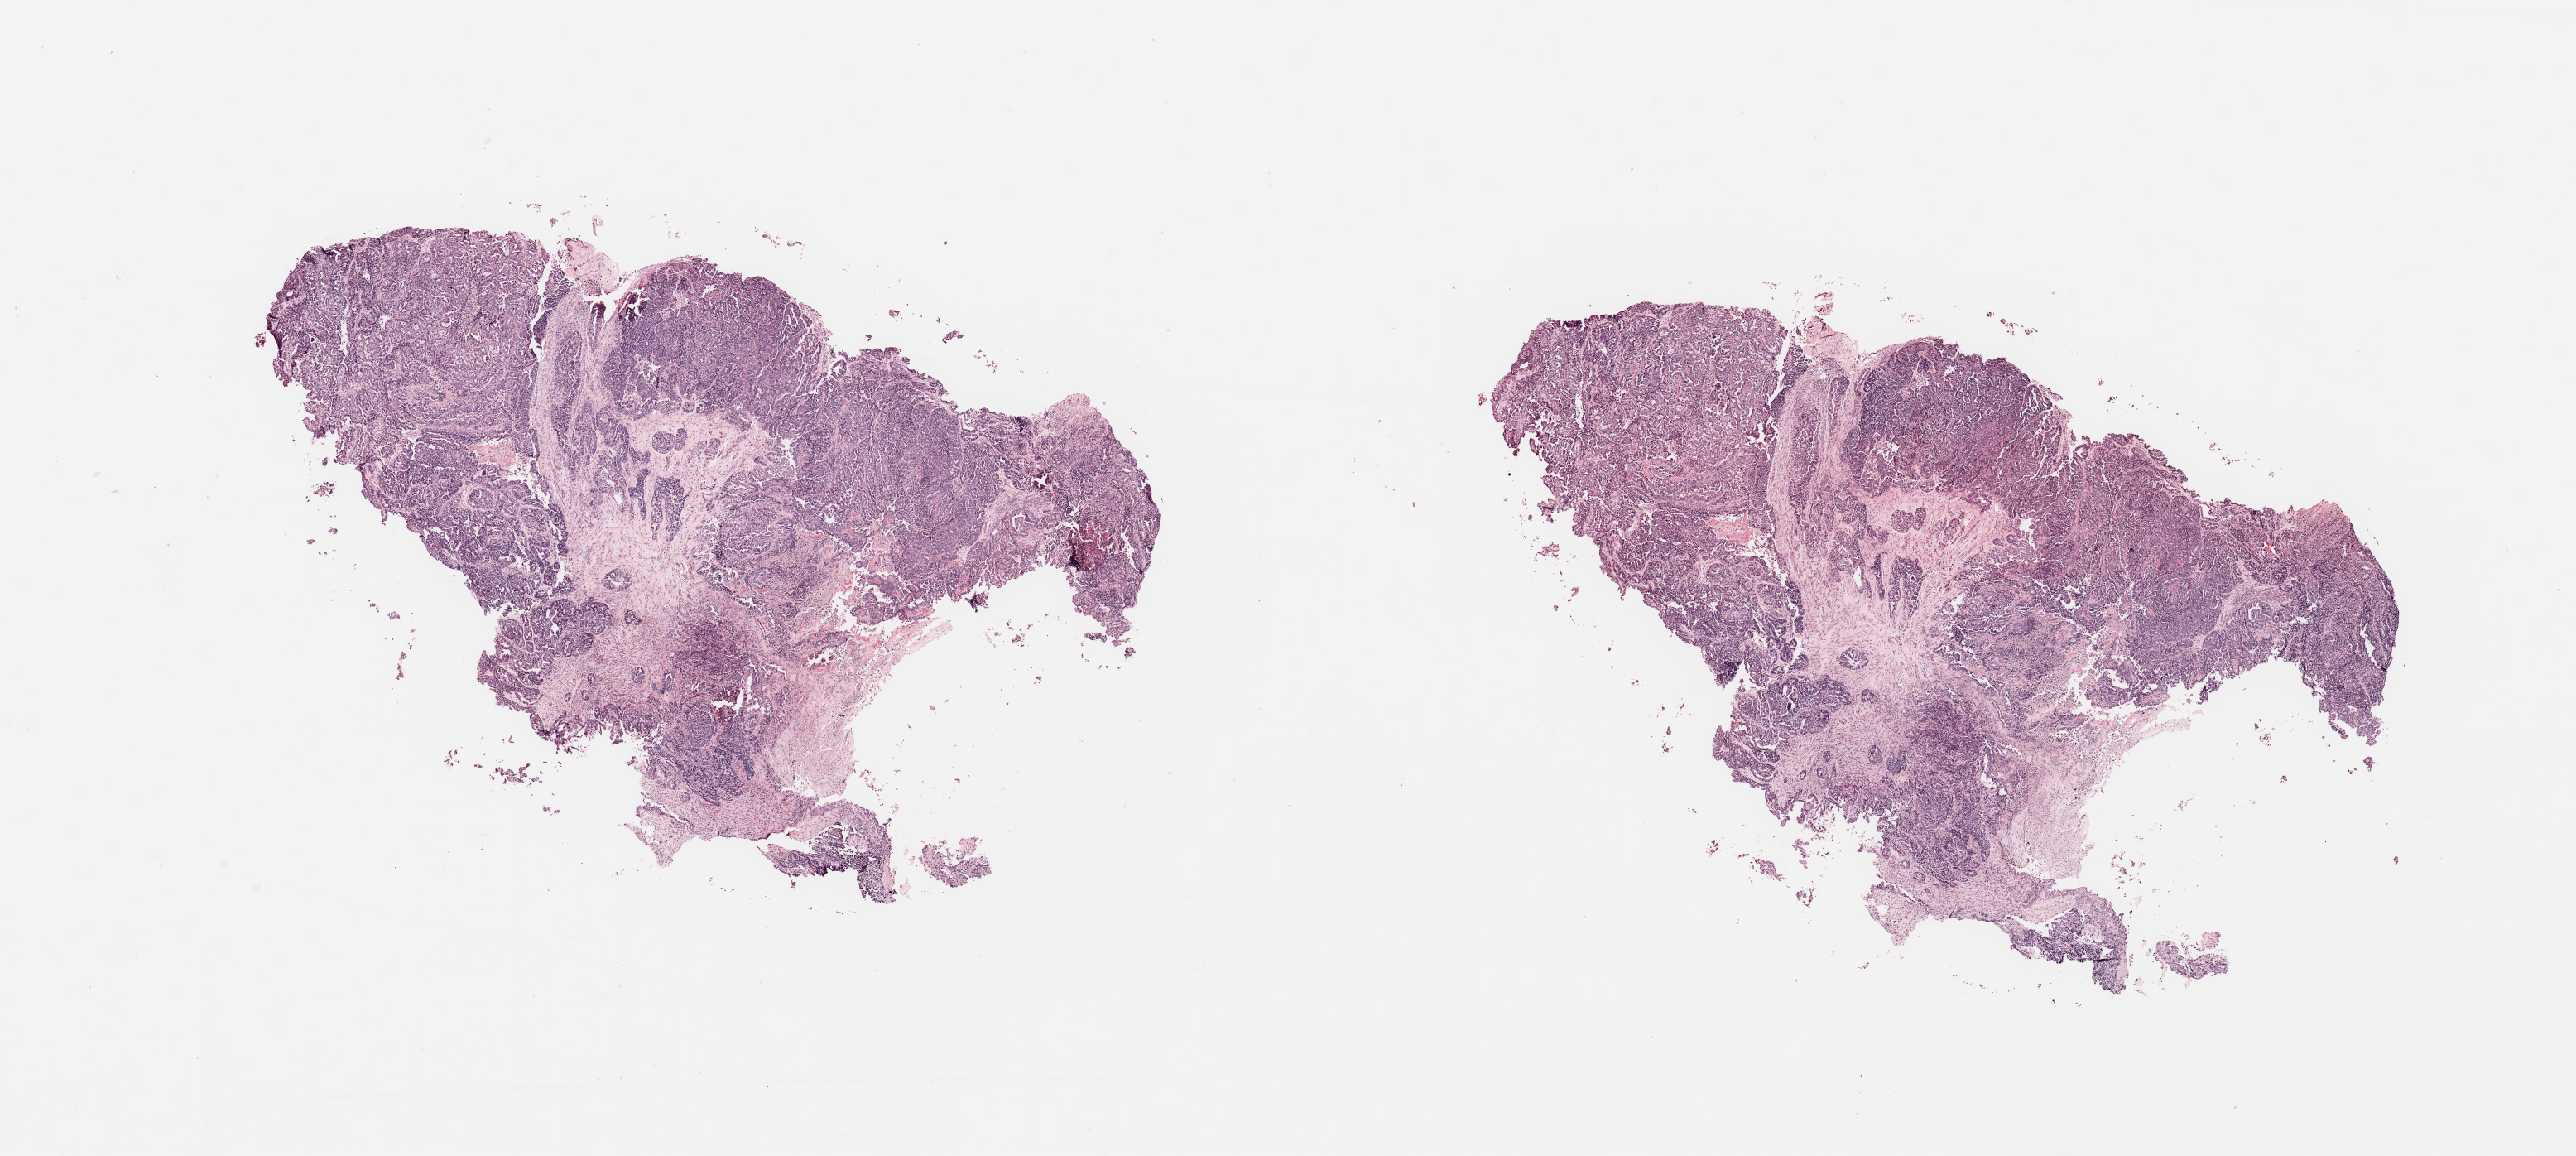
Digitized Hematoxylin and eosin (H&E) stained tissue section (whole slide) — shown as a low-resolution overview of the whole scanned area (about 24.6 x 11.0 mm), tumour tissue sample, uterus. Female, 81 y/o.
* patient diagnosis (cohort enrolment): corpus endometrial carcinoma (uterus)